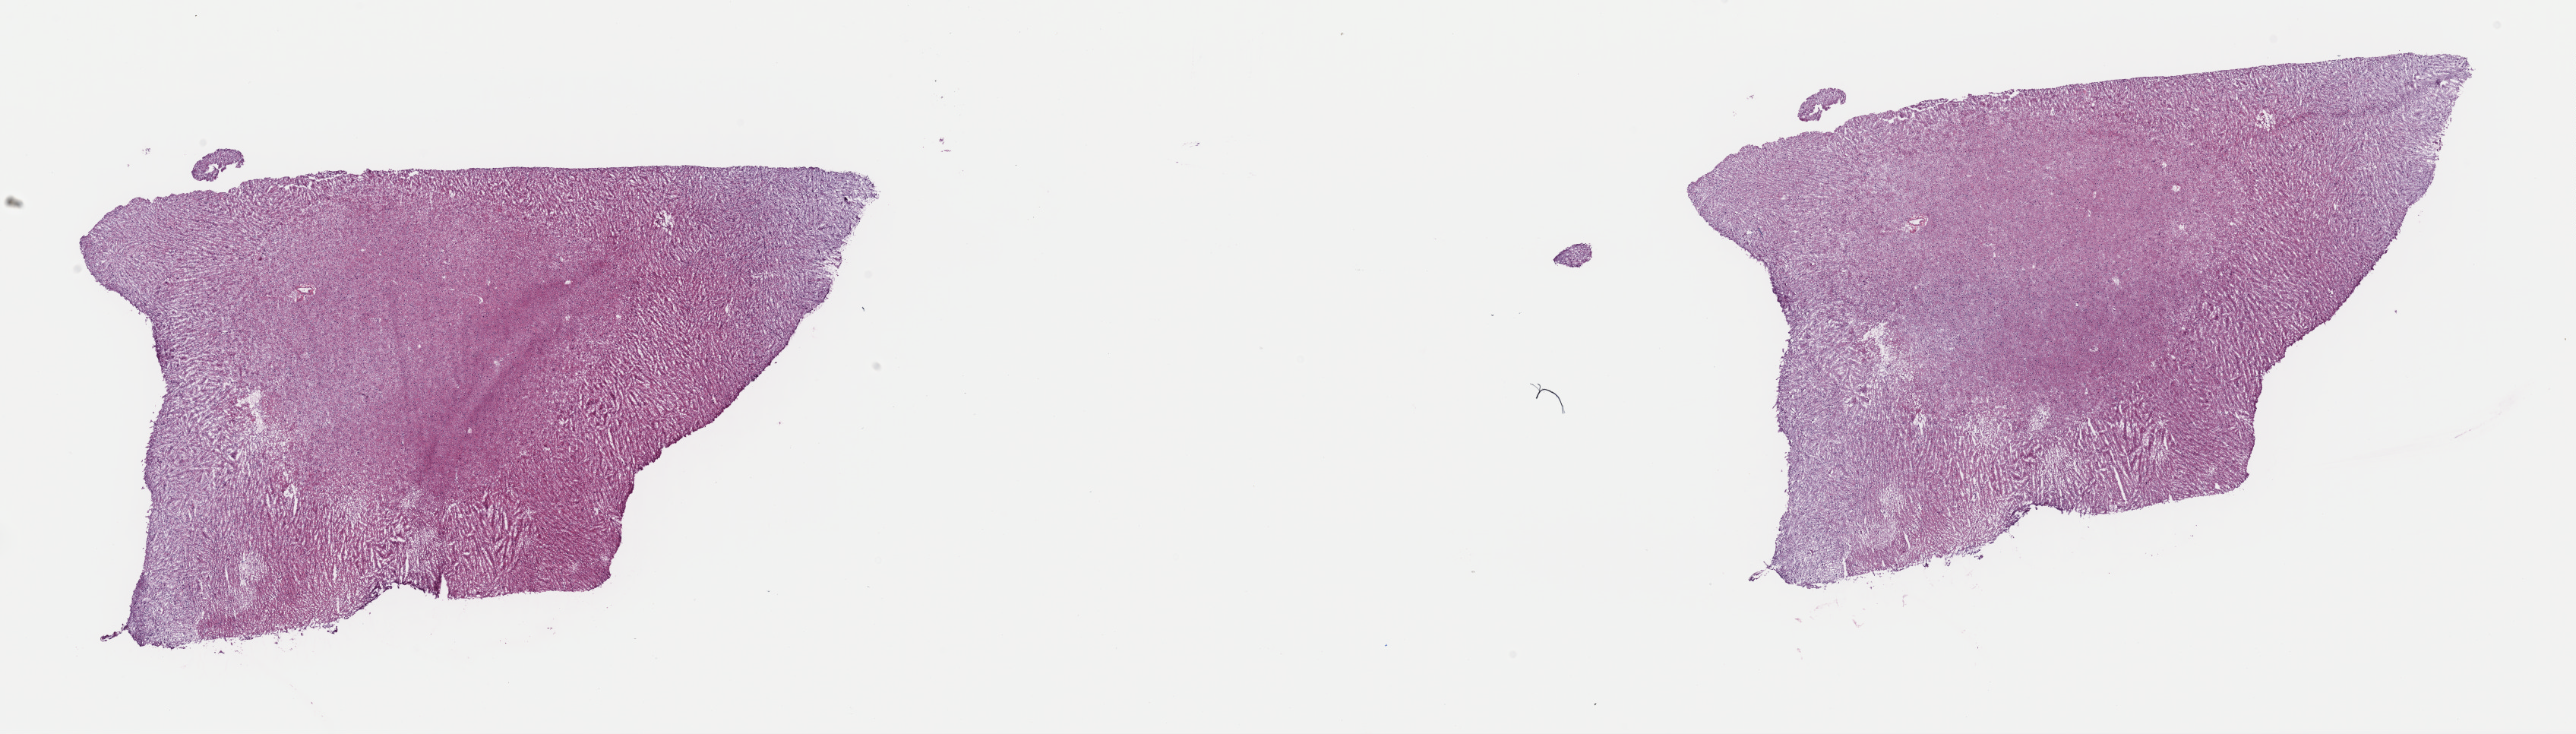
Whole-slide histology image, H&E, a low-resolution overview of the entire scanned area, about 26.8 x 7.6 mm (acquisition: 40x scan). Frozen section. Primary tumour sample from the brain. Patient: female, age at initial diagnosis 58 years. Histologic grade: G2 (moderately differentiated). Slide review estimates, as recorded: tumour cells 40%, tumour nuclei 80%, normal cells 10%, stromal cells 50%, necrosis 0%. Inflammatory infiltration, as recorded: lymphocyte infiltration 2%, monocyte infiltration 2%, neutrophil infiltration 0%.
Pathologic diagnosis: Mixed glioma.